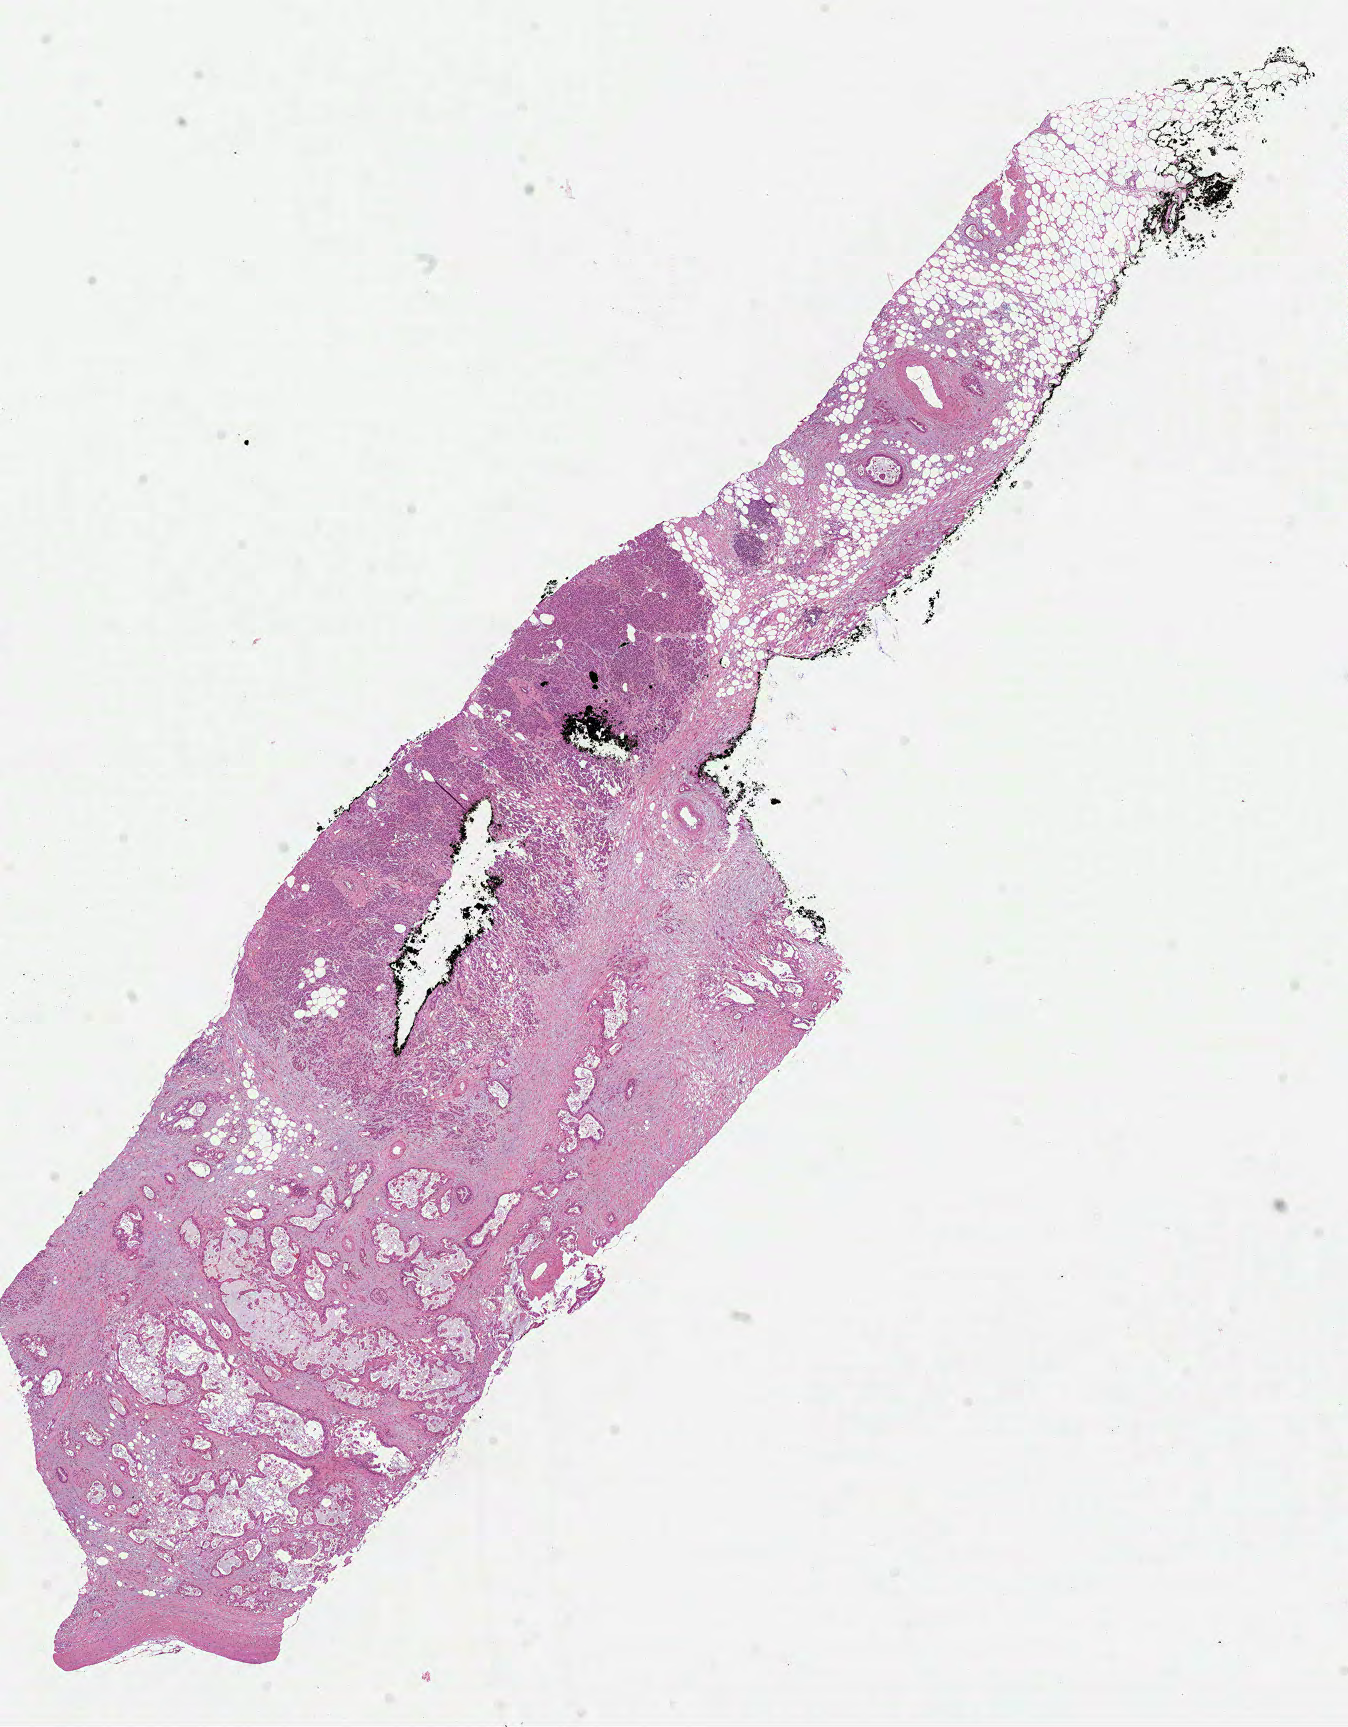
Whole-slide histology image, H&E-stained, a low-resolution overview of the entire scanned area, about 10.9 x 13.9 mm (acquisition: 40x scan), formalin-fixed paraffin-embedded (FFPE) diagnostic section, primary tumour sample from the pancreas. Male patient; age at initial diagnosis 75 years. Histologic grade: G3 (poorly differentiated).
• AJCC pathologic stage: IIB (7th edition)
• lymph nodes positive (case pathology): 4 of 10 examined
• diagnosis: Infiltrating duct carcinoma, NOS (head of pancreas)